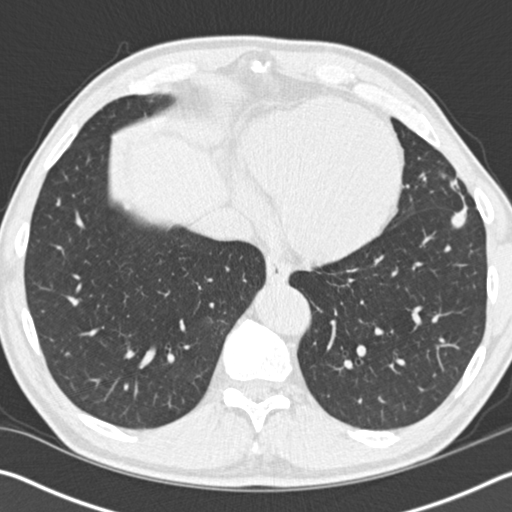
Low-dose screening chest CT, one axial slice. Slice 42 of 162 in the series (ordered by position). Reconstruction kernel B30f. Lung window (W 1500 / L -600 HU). 512 × 512 image matrix.
Structures marked on this image (manually delineated by an expert):
- lesion 1 (tumor, upper lobe of left lung): bounding box [x1, y1, x2, y2] px = [450, 179, 468, 228]